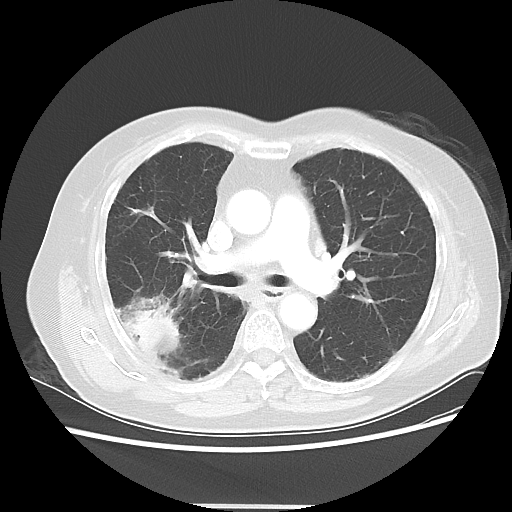
Chest CT, one axial slice; position 29 of 50 along the scan axis; reconstruction kernel LUNG; lung window (W 1500 / L -600 HU); 5 mm slice thickness; 512 × 512 image matrix, field of view 360 × 360 mm. Female patient, age 72 years. Case-level facts recorded for this patient, not image findings: clinical TNM (as recorded): T2 N1 M0.
Annotated regions visible in this slice (bounding box drawn by a radiologist):
- lung tumour (recorded histology: adenocarcinoma): bounding box (x1, y1, x2, y2) in pixels: (124, 302, 181, 353)